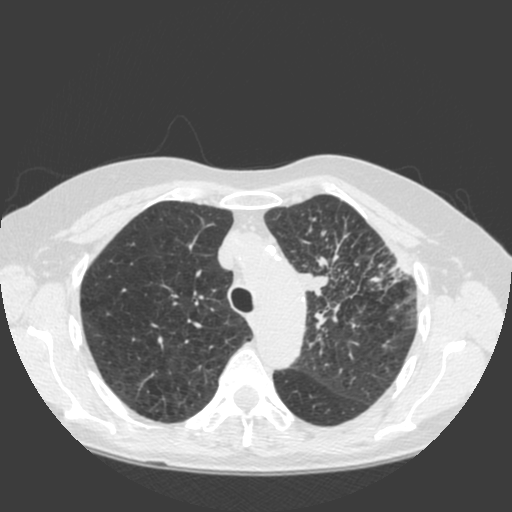
Low-dose screening chest CT, axial slice, baseline screening round, lung window (W 1500 / L -600 HU), 2 mm slice thickness, standard (soft-tissue) reconstruction kernel (C), 512 × 512 image matrix, field of view 350 × 350 mm. Female participant, aged 66 years at enrolment.
• Expert reader's lesion annotation, bounding box (x1, y1, x2, y2) in pixels: (287, 248, 396, 345).
• Screening reader's record for this exam (one nodule recorded; not confirmed to be the boxed lesion): non-calcified nodule or mass ≥4 mm, left upper lobe, 61 × 45 mm, spiculated (stellate) margins, soft tissue attenuation.
• Official screen result: positive, change unspecified: nodule(s) >= 4 mm or enlarging nodule(s), mass(es), or other non-specific abnormalities suspicious for lung cancer.
• Later outcome: lung cancer diagnosed 19 days after this screen — squamous cell carcinoma, keratinizing, NOS, left upper lobe, left hilum, mediastinum, left main stem bronchus, other location, poorly differentiated (G3), stage IIIB (AJCC 6th edition), 60 mm at pathology.